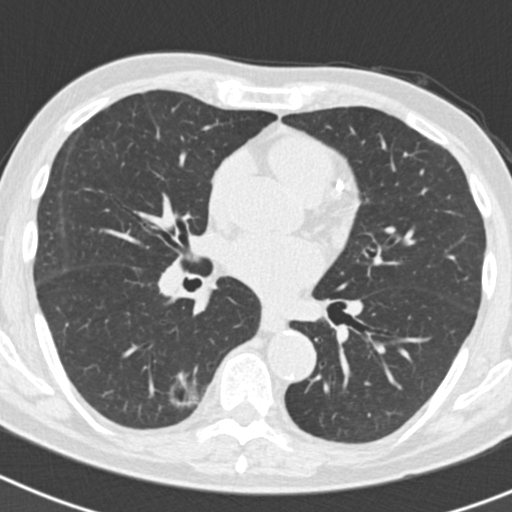
Chest CT (low-dose screening protocol), one axial image; second annual screen; lung window (W 1500 / L -600 HU); 2 mm slice thickness; standard (soft-tissue) reconstruction kernel (B30f); slice 88 of 186 in the series. Male, age 70 years at enrolment. Current smoker at enrolment.
Expert reader's lesion annotation, bounding box [x1, y1, x2, y2] px = [128, 365, 204, 431]. The screening reader recorded 5 non-calcified nodules or masses ≥4 mm on this exam (right lower lobe, right lower lobe, right upper lobe, right upper lobe, left upper lobe); which of them this box marks is not recorded. Official screen result: positive, other. Lung cancer was diagnosed 622 days after this screen: bronchiolo-alveolar adenocarcinoma, NOS, right lower lobe, poorly differentiated (G3), stage IB (AJCC 6th edition), 30 mm at pathology.